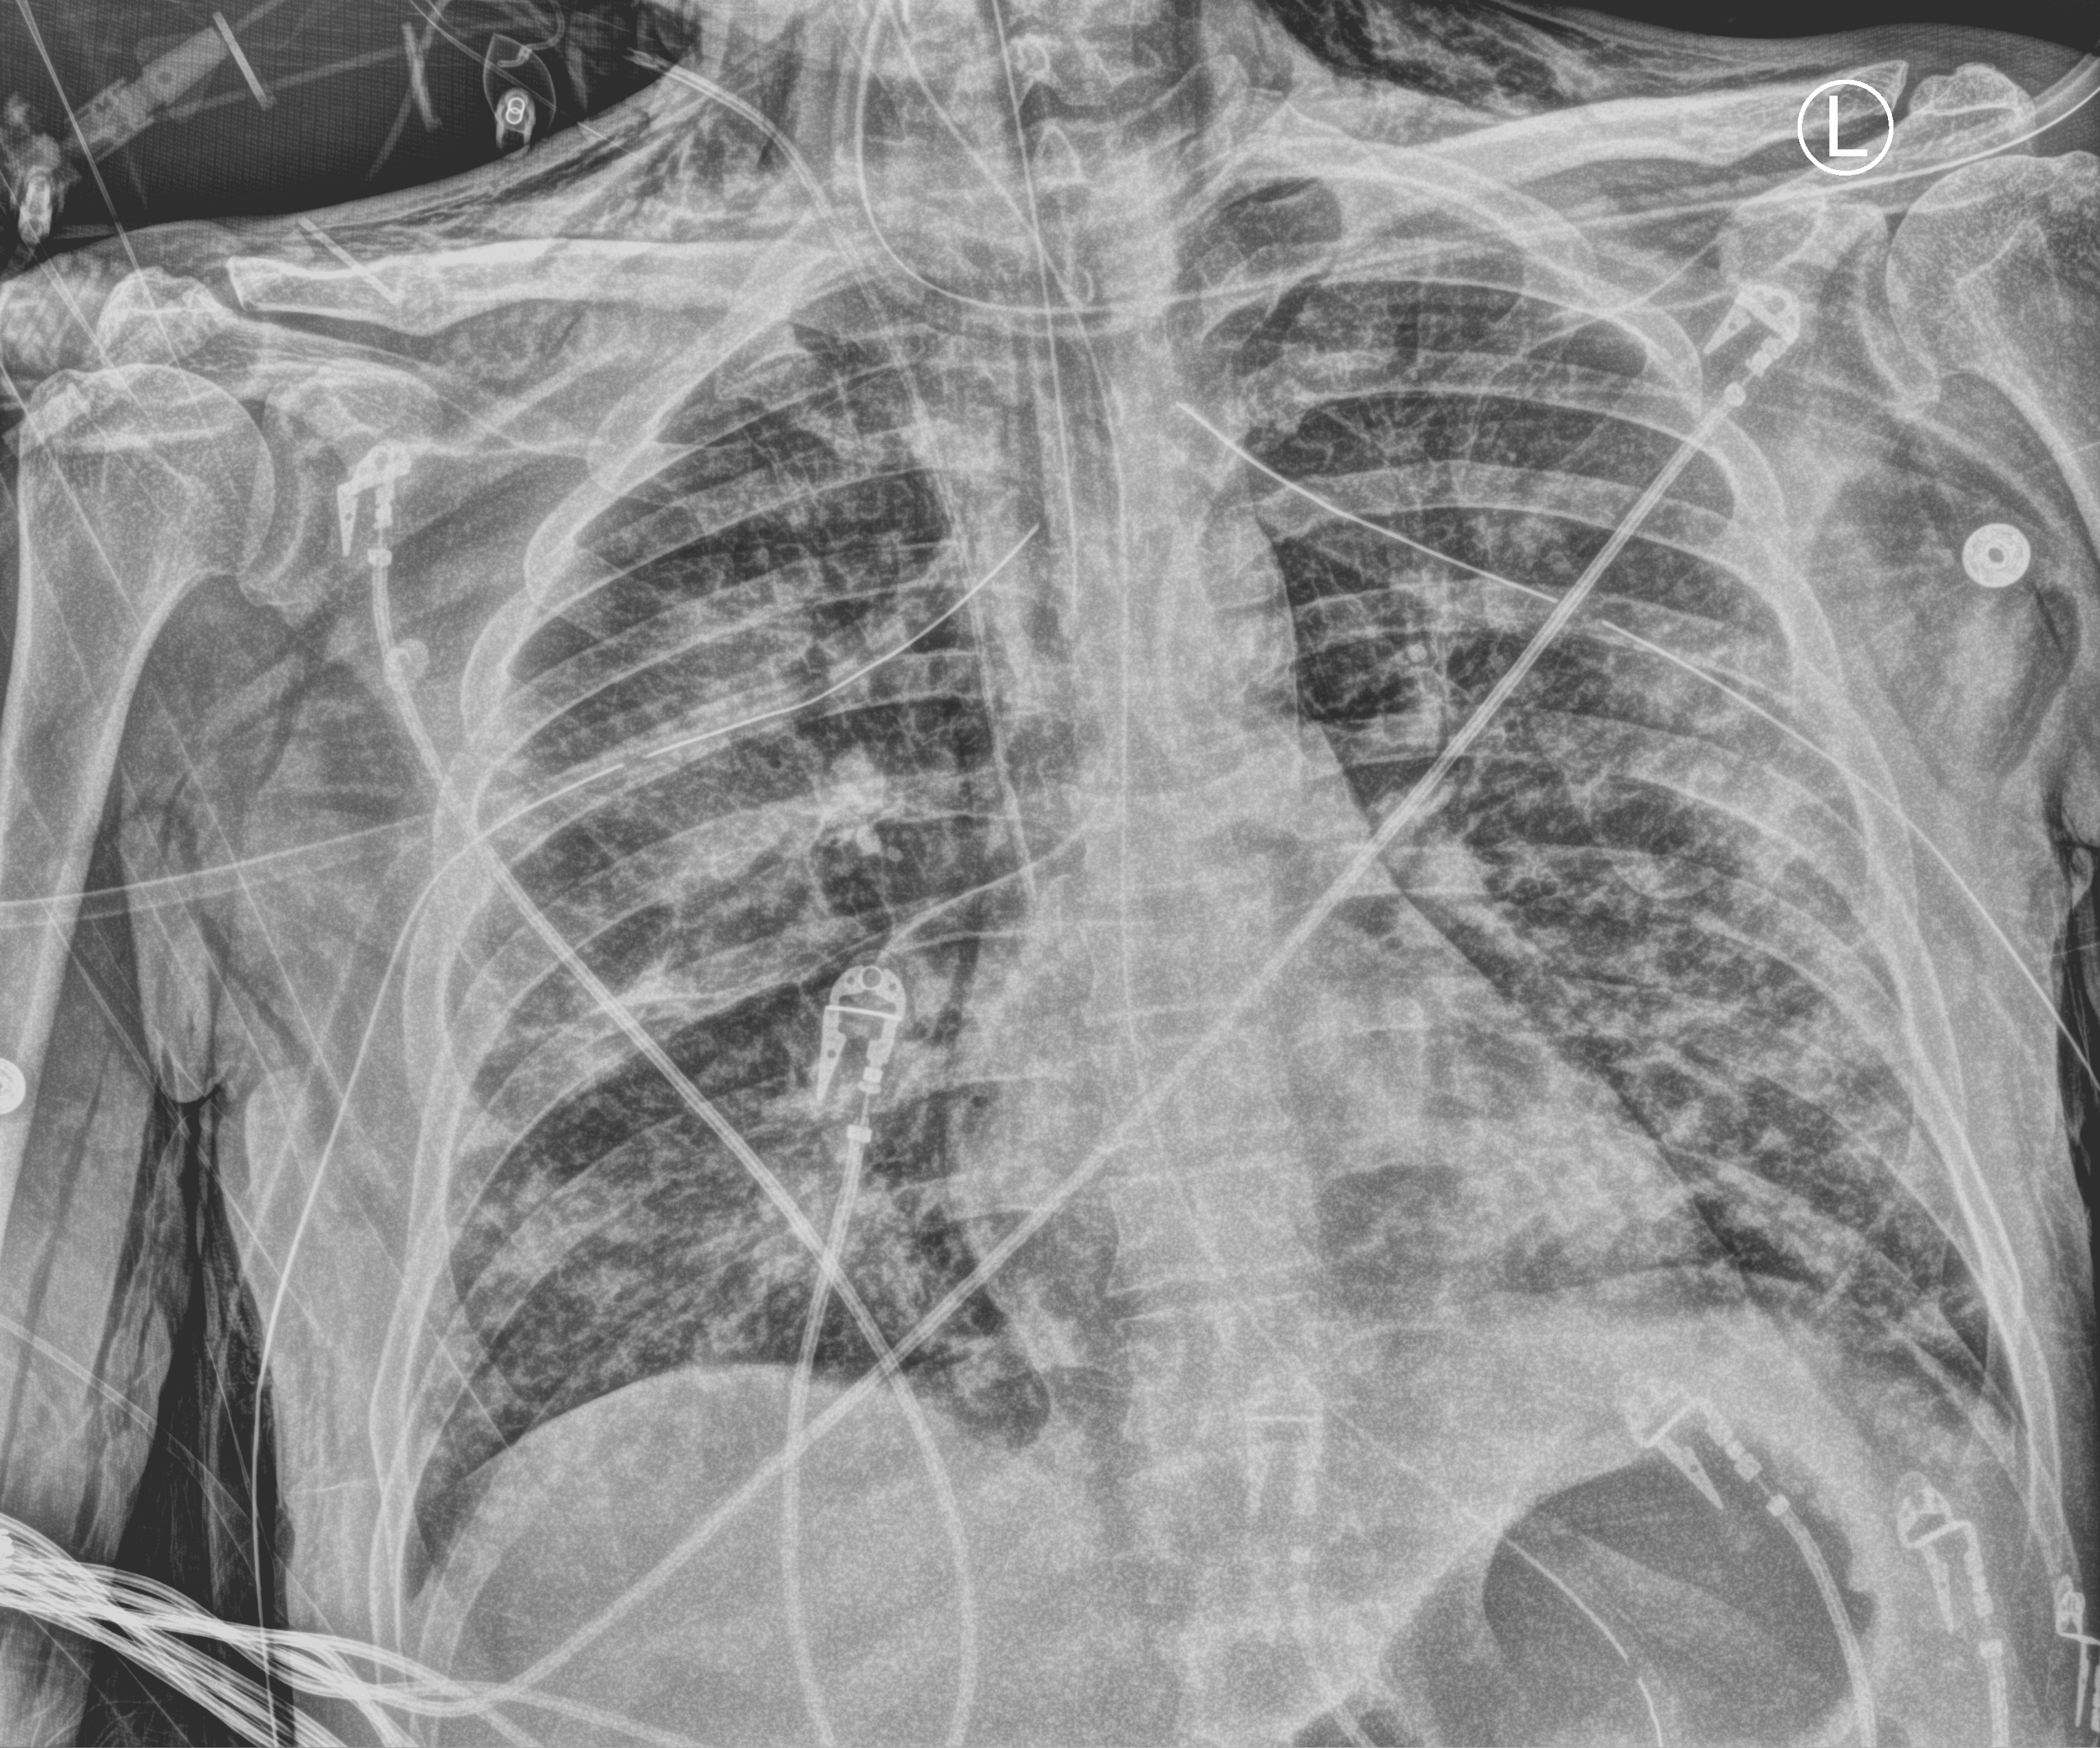
Bedside chest radiograph (computed radiography). Male patient hospitalised with COVID-19, age 18–59 years.
Admission-level facts for this patient (not findings on this image; timing relative to this image not recorded): chronic kidney disease (admission record): no; admitted to intensive care during this hospital stay: yes.